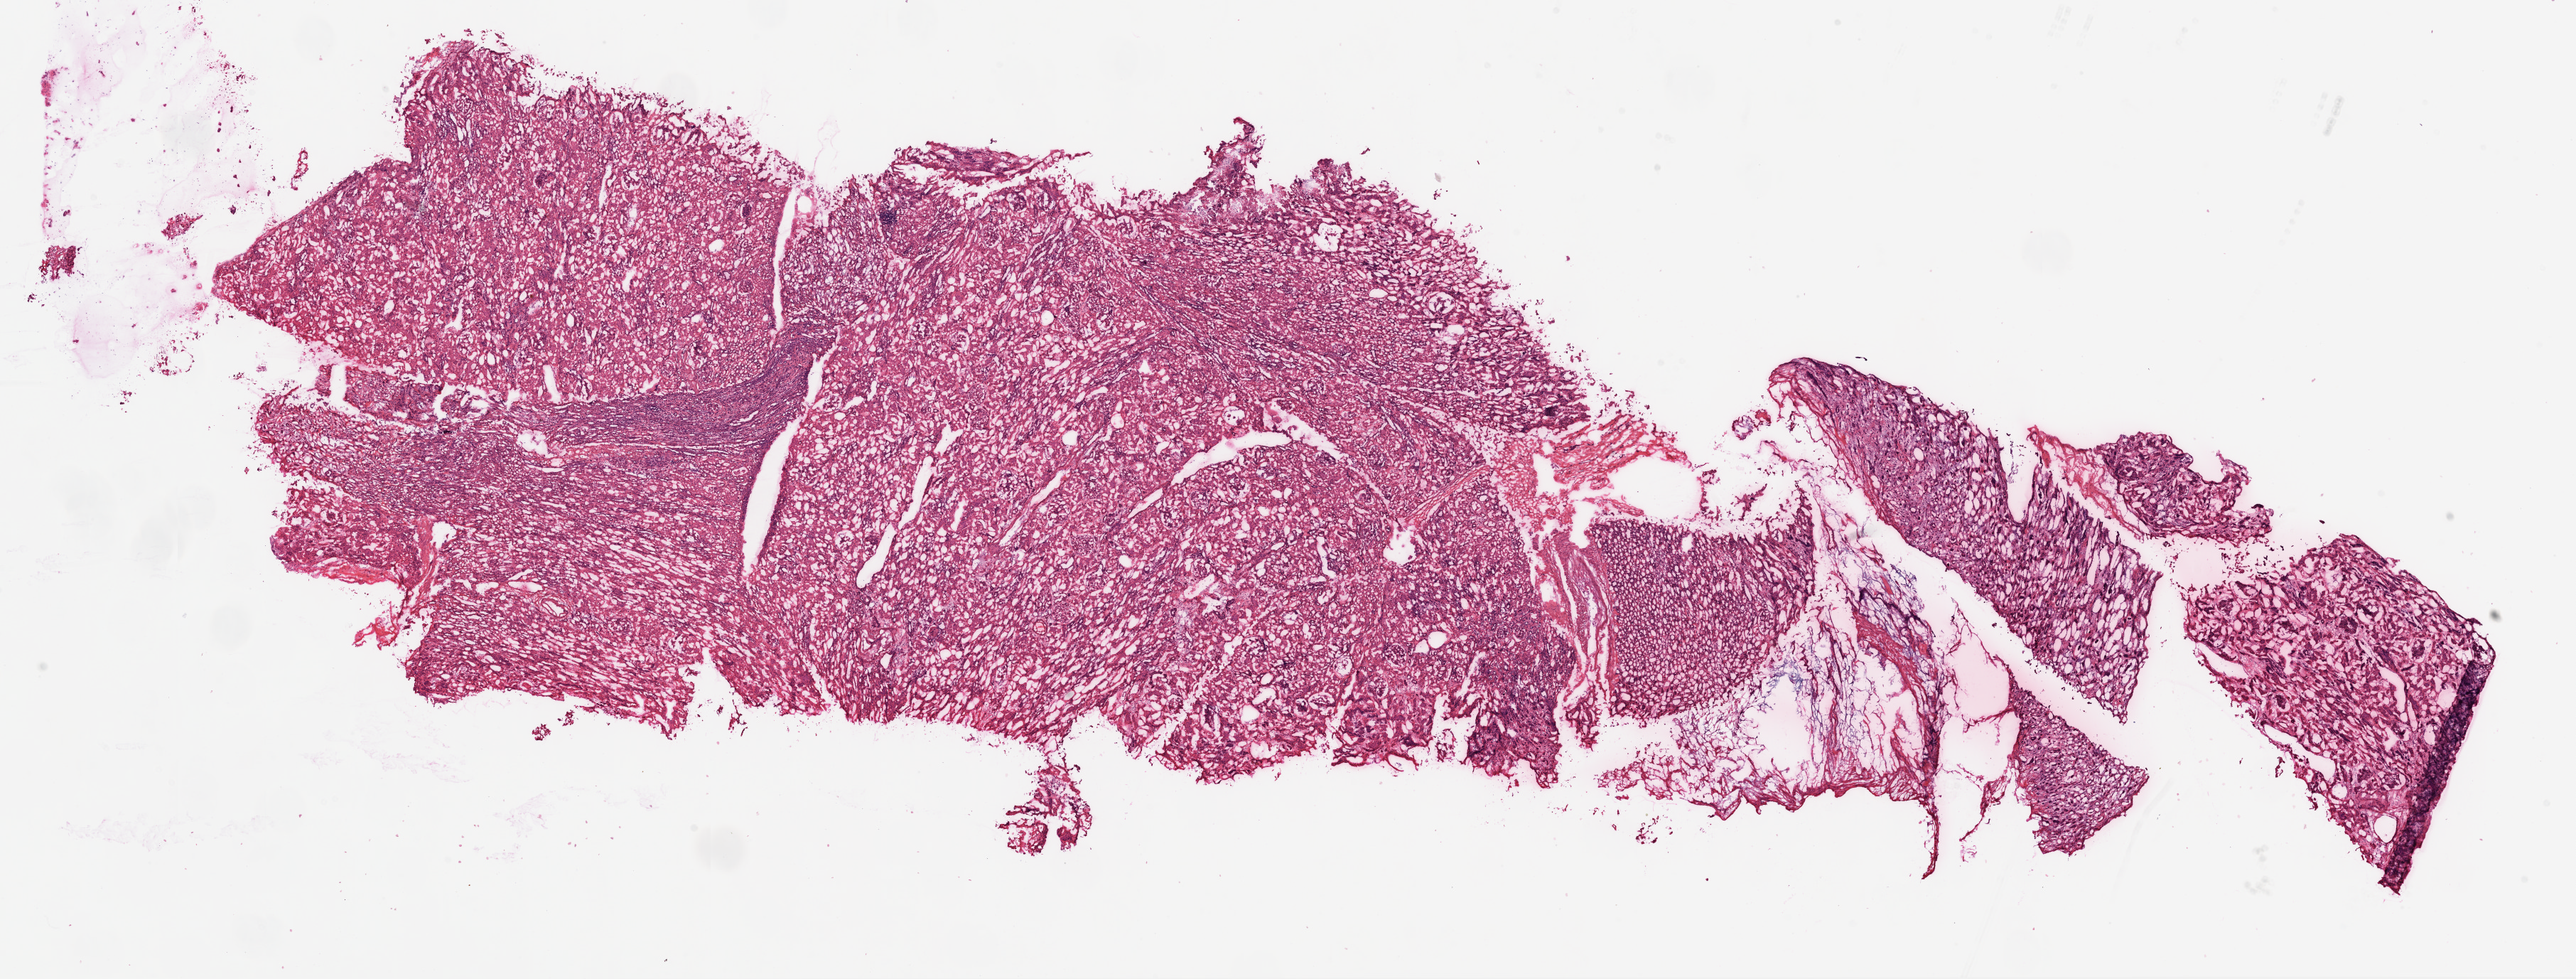
Whole-slide histology image, Hematoxylin and eosin (H&E) stained — a low-resolution overview of the entire scanned area, about 29.1 x 11.0 mm (from a 20x scan); frozen section; kidney, solid tissue normal (non-tumour tissue) sample. Female patient; age at initial diagnosis 63 years.
* this section: solid tissue normal sample (biorepository sample class)
* patient diagnosis: Clear cell adenocarcinoma, NOS